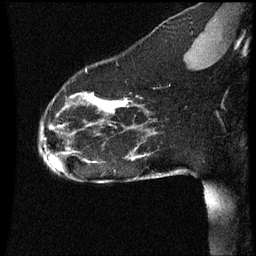
Breast MRI (dynamic contrast-enhanced), one sagittal slice; dynamic contrast-enhanced series, image 2 of 3 at this slice position (ordered by acquisition); 1.5 T; TE 4.2 ms, TR 8.9 ms; 256 × 256 image matrix. Patient: female, 35 years. Case-level facts recorded for this patient, not image findings: setting: breast cancer imaged before/during neoadjuvant chemotherapy; receptor status: HER2-positive.
Annotated regions visible in this slice (semi-automatic segmentation, software-assisted and operator-edited):
- analysis volume of interest (the breast-tissue region the enhancement analysis was run in; not a lesion): bounding box <37,66,177,177> (left, top, right, bottom; pixels)
- tumour enhancement mask (voxels above the 70 % enhancement threshold inside the analysis volume of interest): <62,98,129,127>